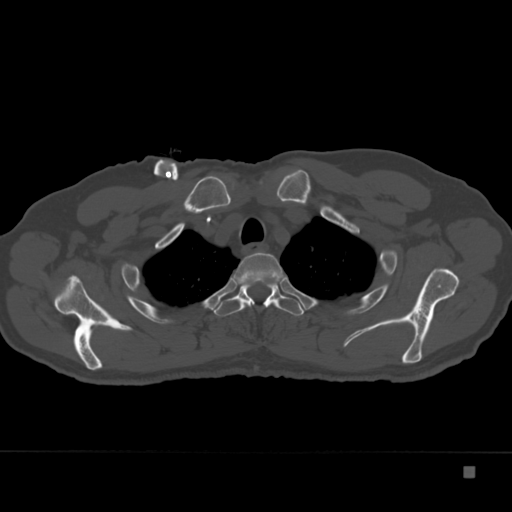
CT including the spine, one axial slice; position 292 of 332 along the scan axis; 120 kVp; bone window (W 1800 / L 400 HU); 1.5 mm slice thickness; 512 × 512 image matrix. Patient: male, 72 years. Case-level facts recorded for this patient, not image findings: primary cancer: skeletal.
Outlined on this slice (semi-automatic segmentation, software-assisted and operator-edited):
- T2 vertebra: bounding box (x1, y1, x2, y2) in pixels: (231, 252, 284, 288)
- T3 vertebra: (214, 280, 304, 316)